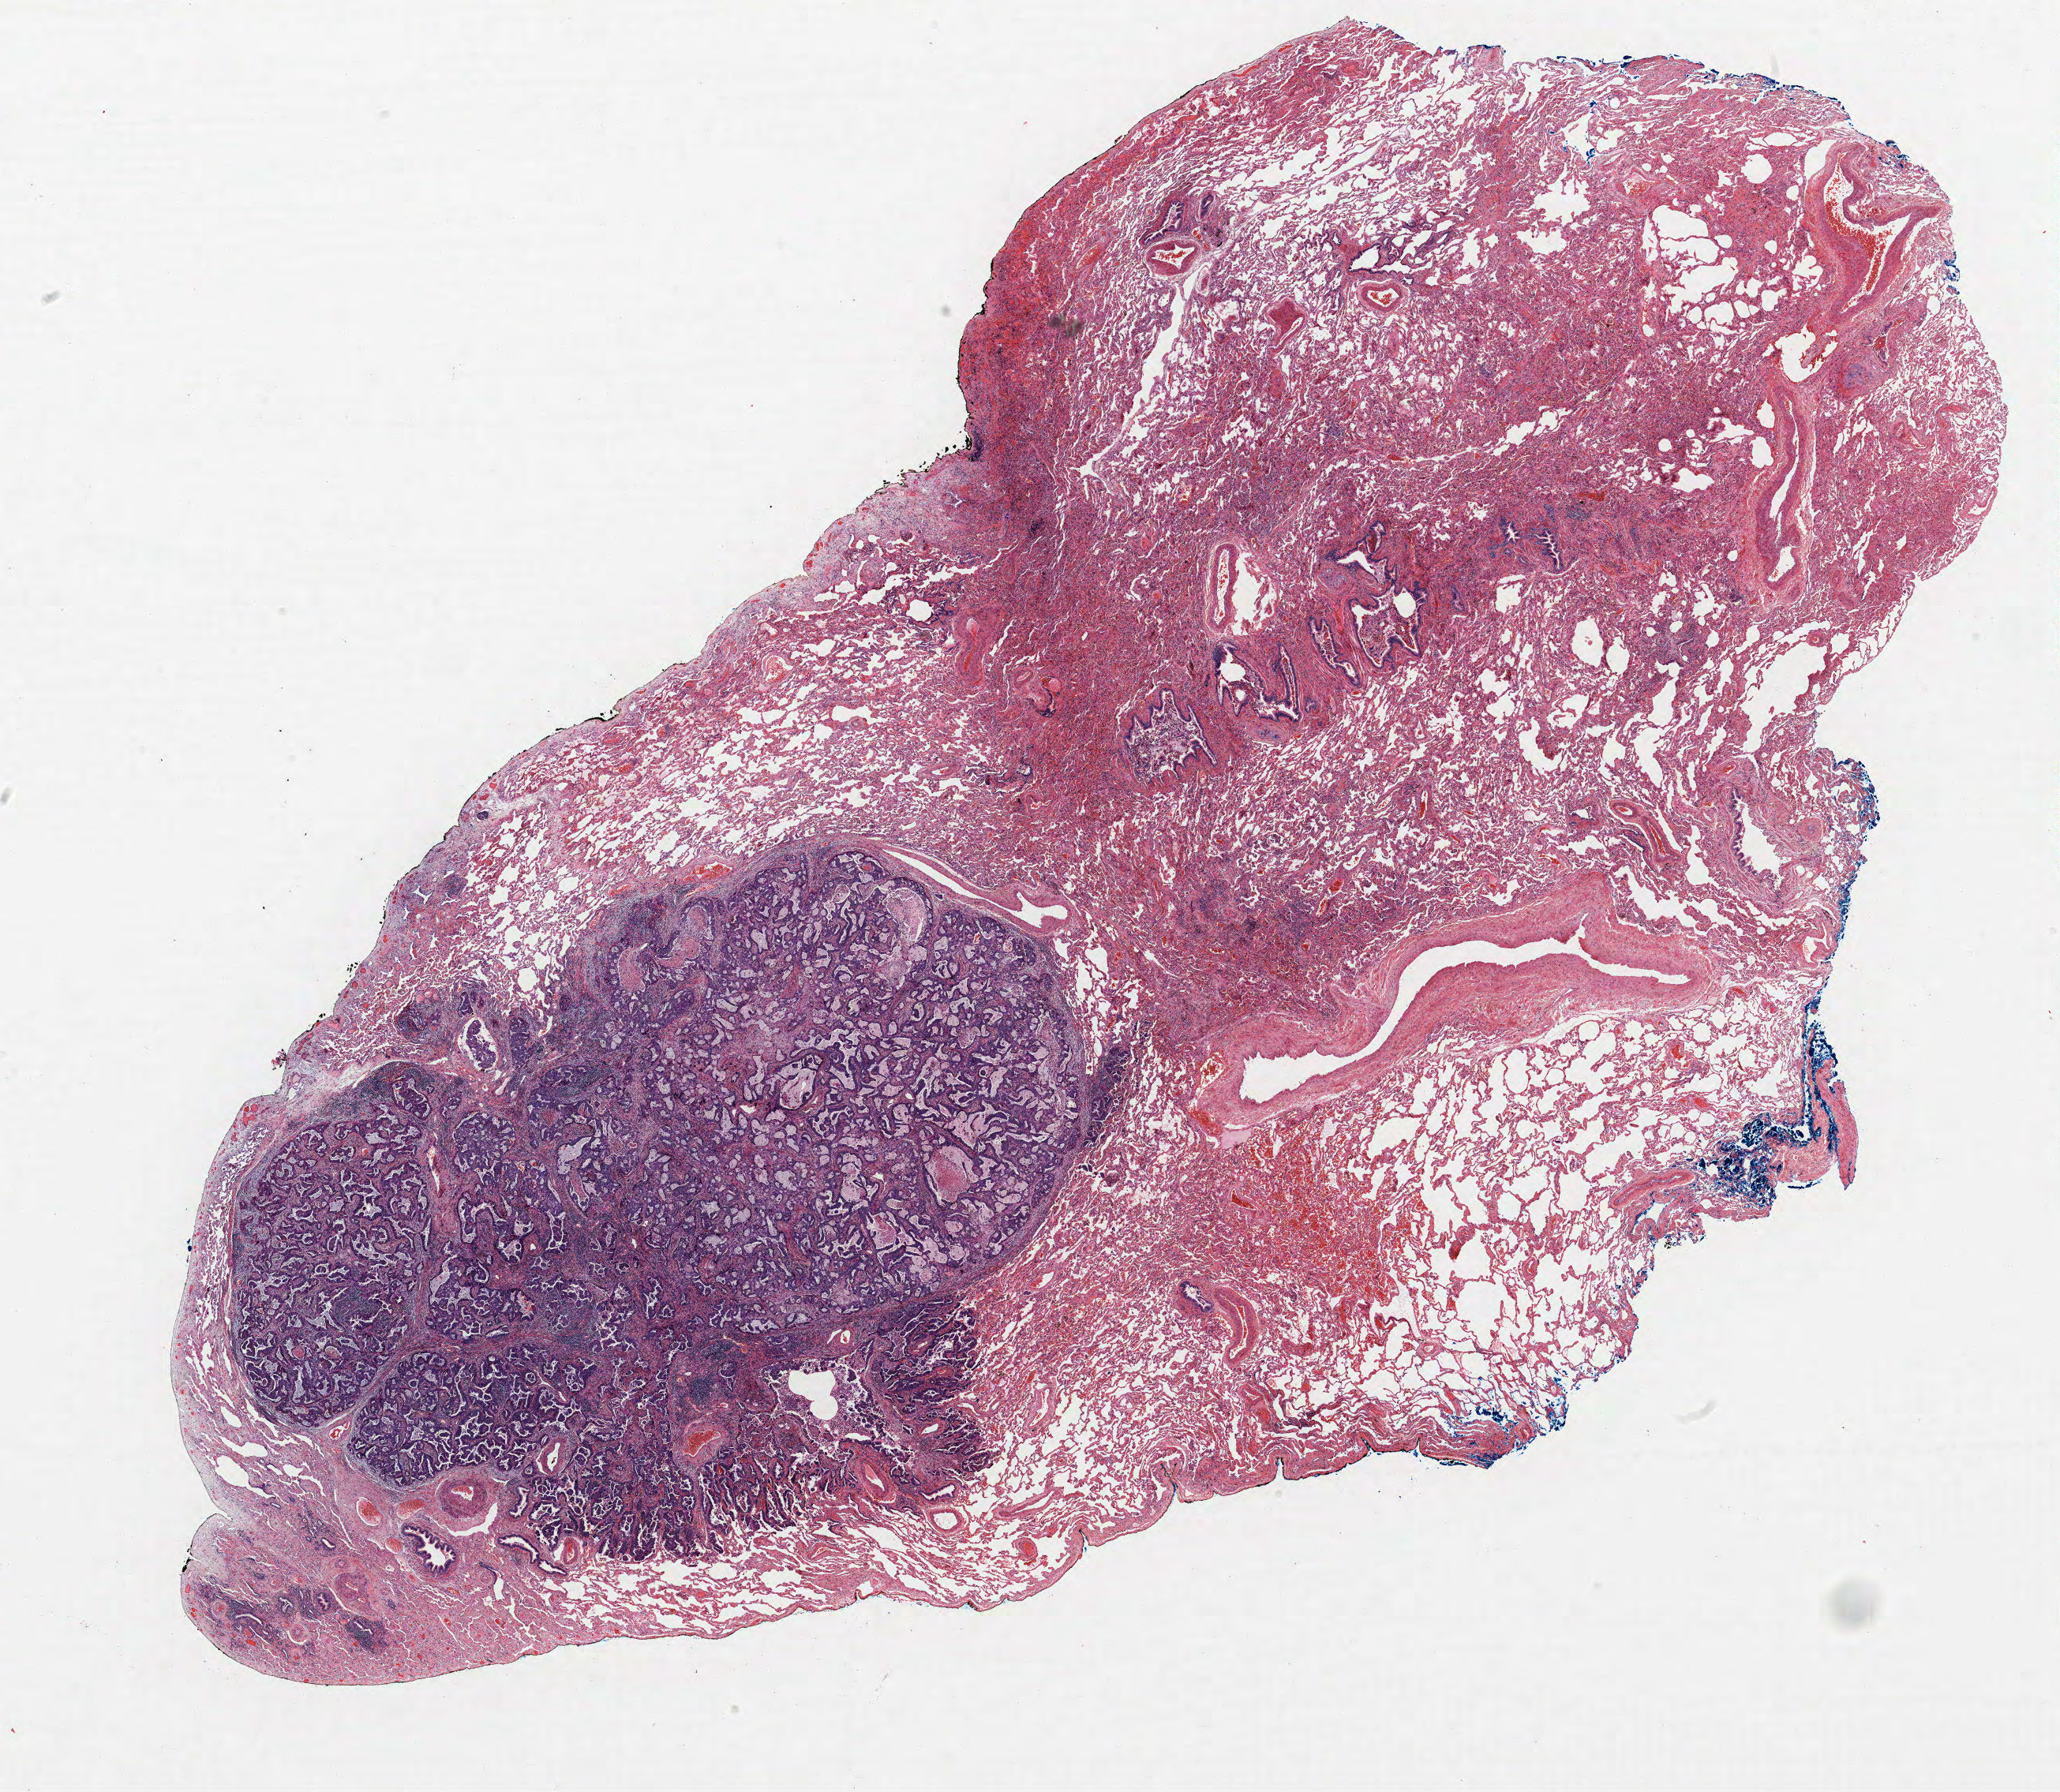
Hematoxylin and eosin (H&E) stained whole-slide image, shown as a low-resolution overview of the whole scanned area (about 20.9 x 18.2 mm, acquisition: 40x scan); formalin-fixed paraffin-embedded (FFPE) section; lung tissue. Male, age 66 at enrolment. Former smoker at enrolment. Grade: moderately differentiated (G2).
Tumour size (pathology): 9 mm. Stage (AJCC 6th edition): IIB. Primary tumour location (clinical record): left upper lobe. ICD-O-3 topography: upper lobe of lung (C34.1). Participant's lung-cancer diagnosis: Adenocarcinoma, NOS.